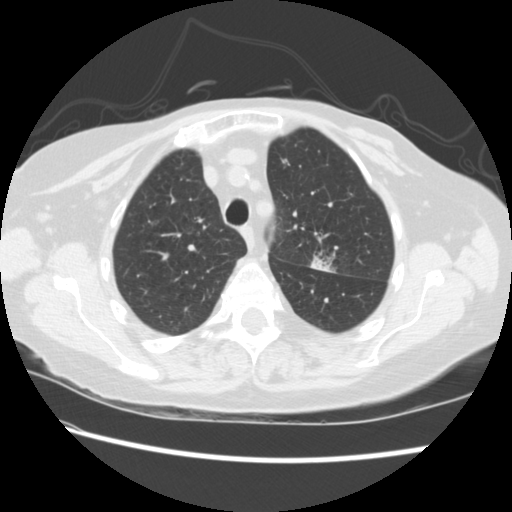
Low-dose screening chest CT, axial slice; baseline screening round; lung window (W 1500 / L -600 HU); 2.5 mm slice thickness; 120 kVp; slice 57 of 224 in the series; 512 × 512 image matrix, field of view 340 × 340 mm. Female, age 74 years at enrolment.
• Lesion marked by an expert reader, bounding box <296,236,346,280> (left, top, right, bottom; pixels).
• The screening reader recorded 2 non-calcified nodules or masses ≥4 mm on this exam (left upper lobe, right lower lobe); which of them this box marks is not recorded.
• Official screen result: positive, change unspecified: nodule(s) >= 4 mm or enlarging nodule(s), mass(es), or other non-specific abnormalities suspicious for lung cancer.
• Later outcome: lung cancer diagnosed 309 days after this screen — non-small cell carcinoma, left upper lobe, stage IV (AJCC 6th edition).